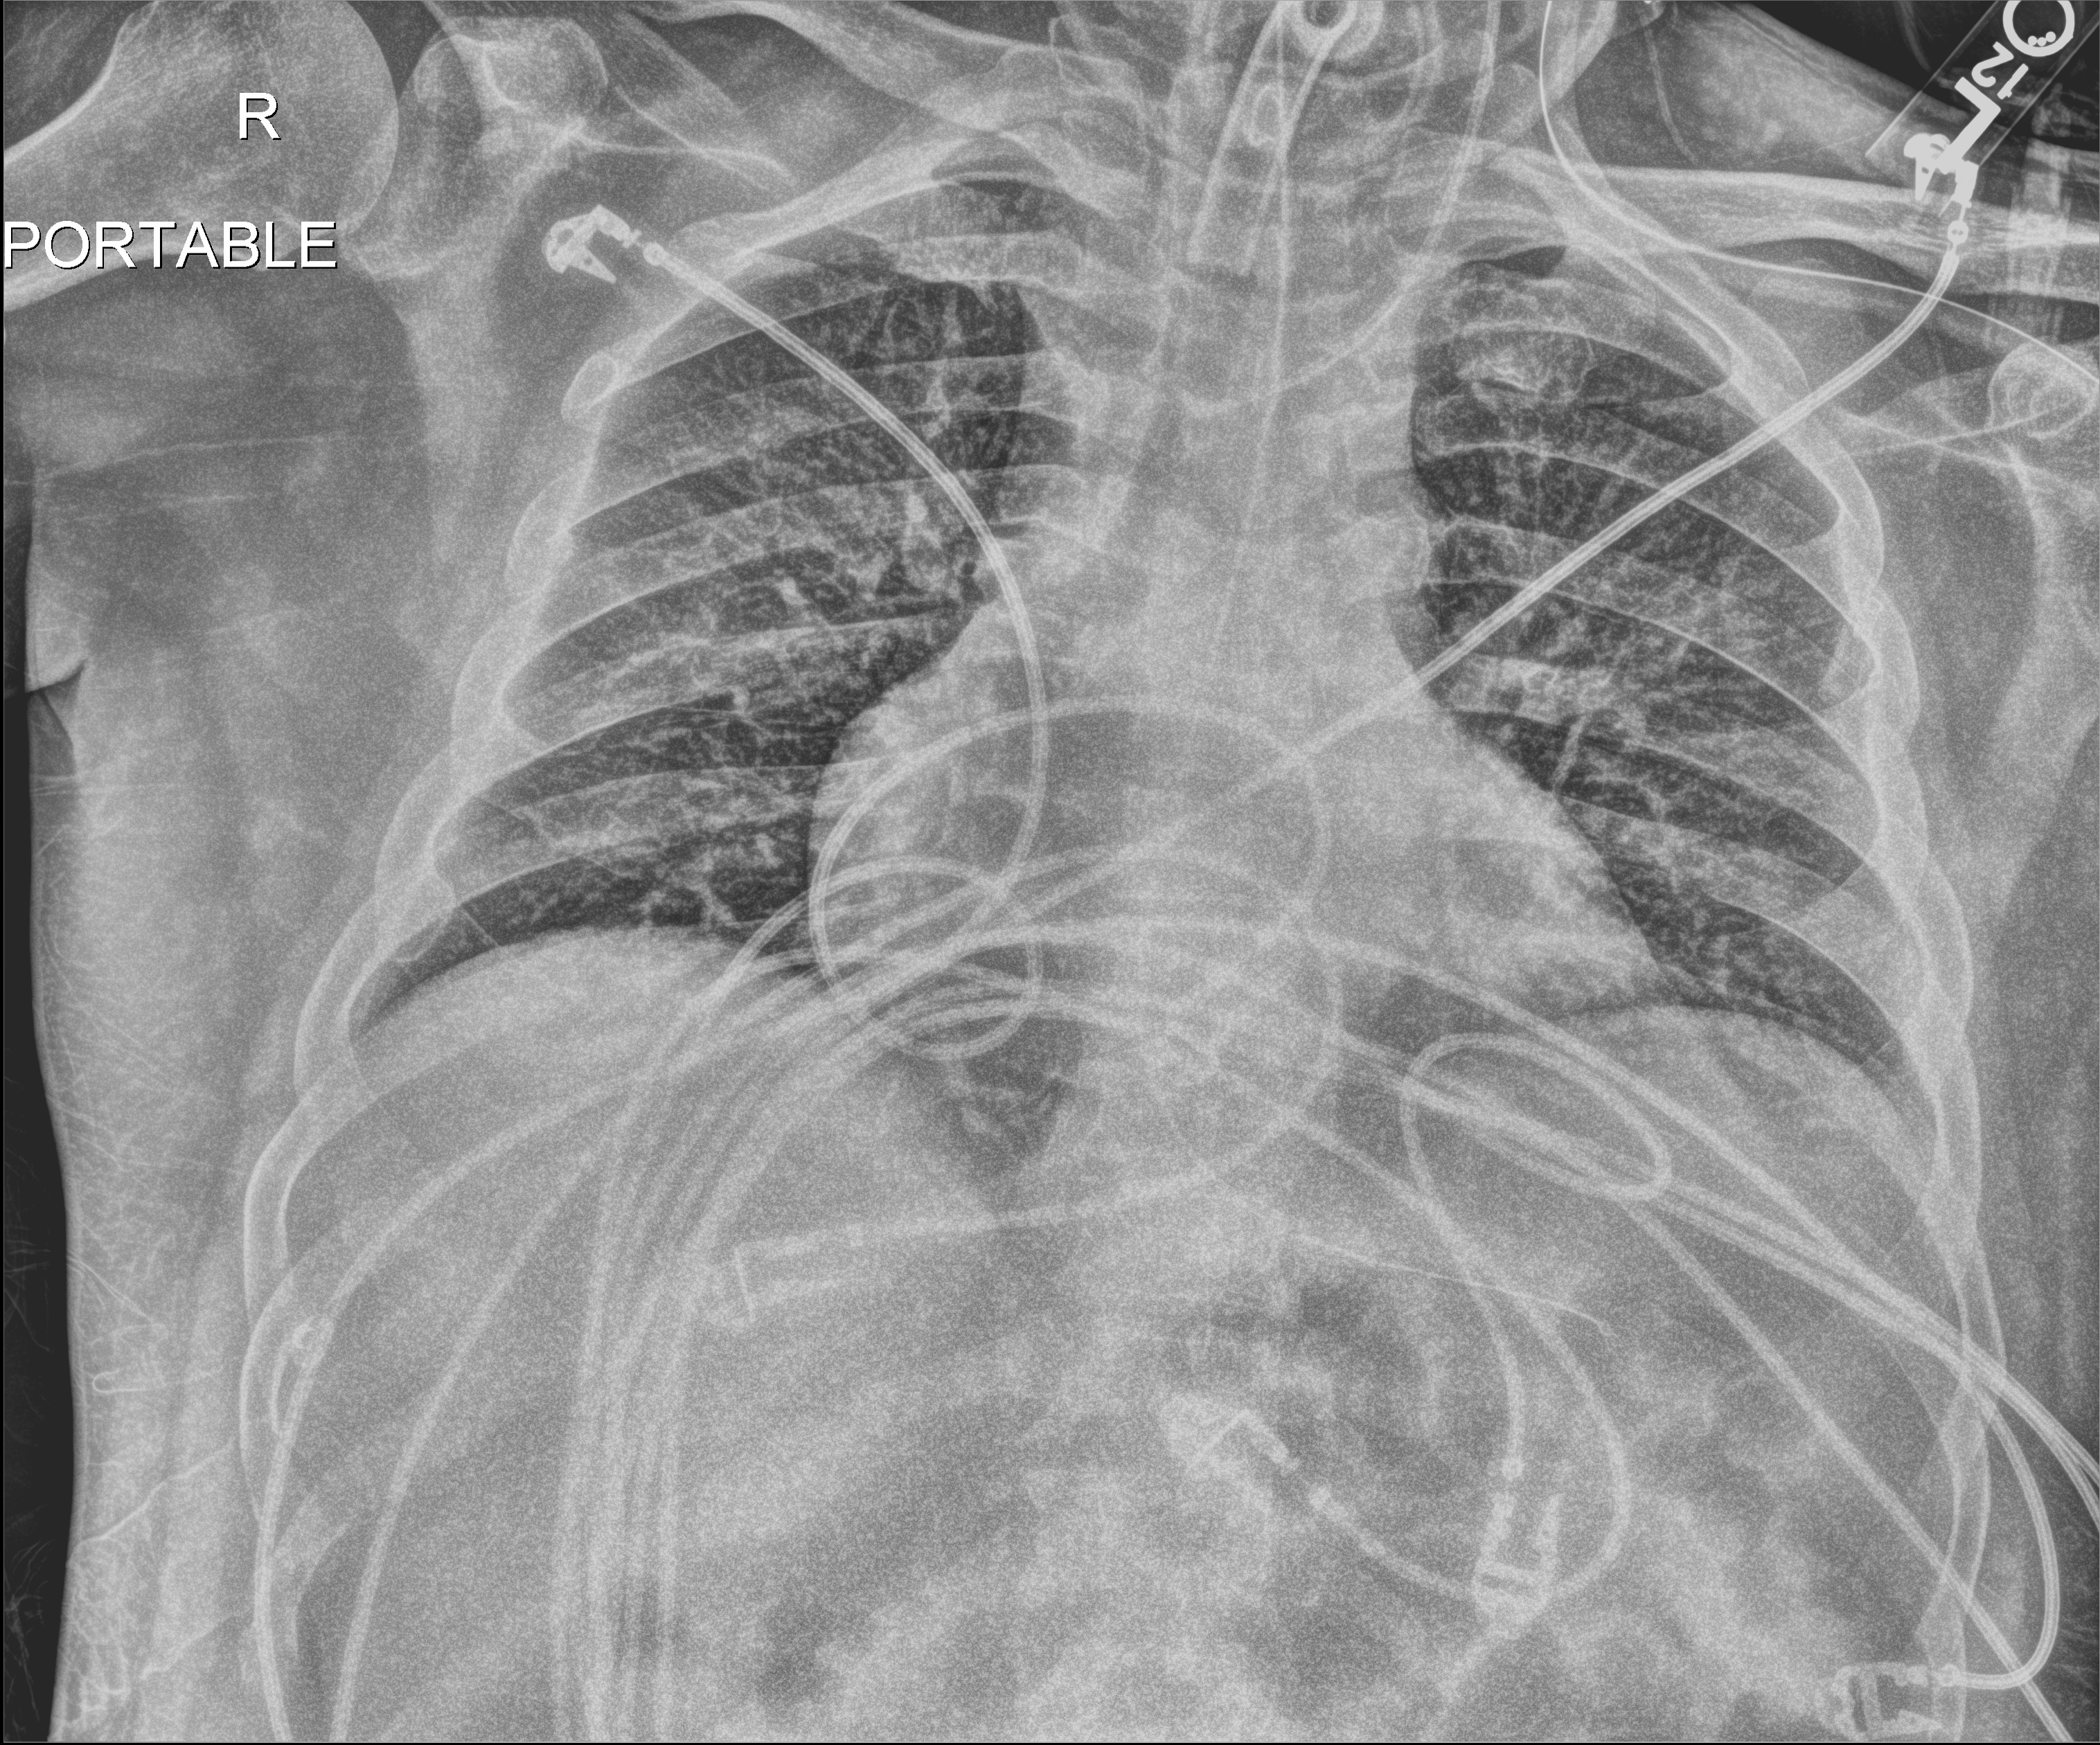
Chest X-ray (portable), anteroposterior (AP) projection. Patient hospitalised with COVID-19; male, aged 18–59 years.
Hospital-stay facts (about this admission, not read from this image; timing relative to this image not recorded):
- mechanically ventilated during this hospital stay: yes